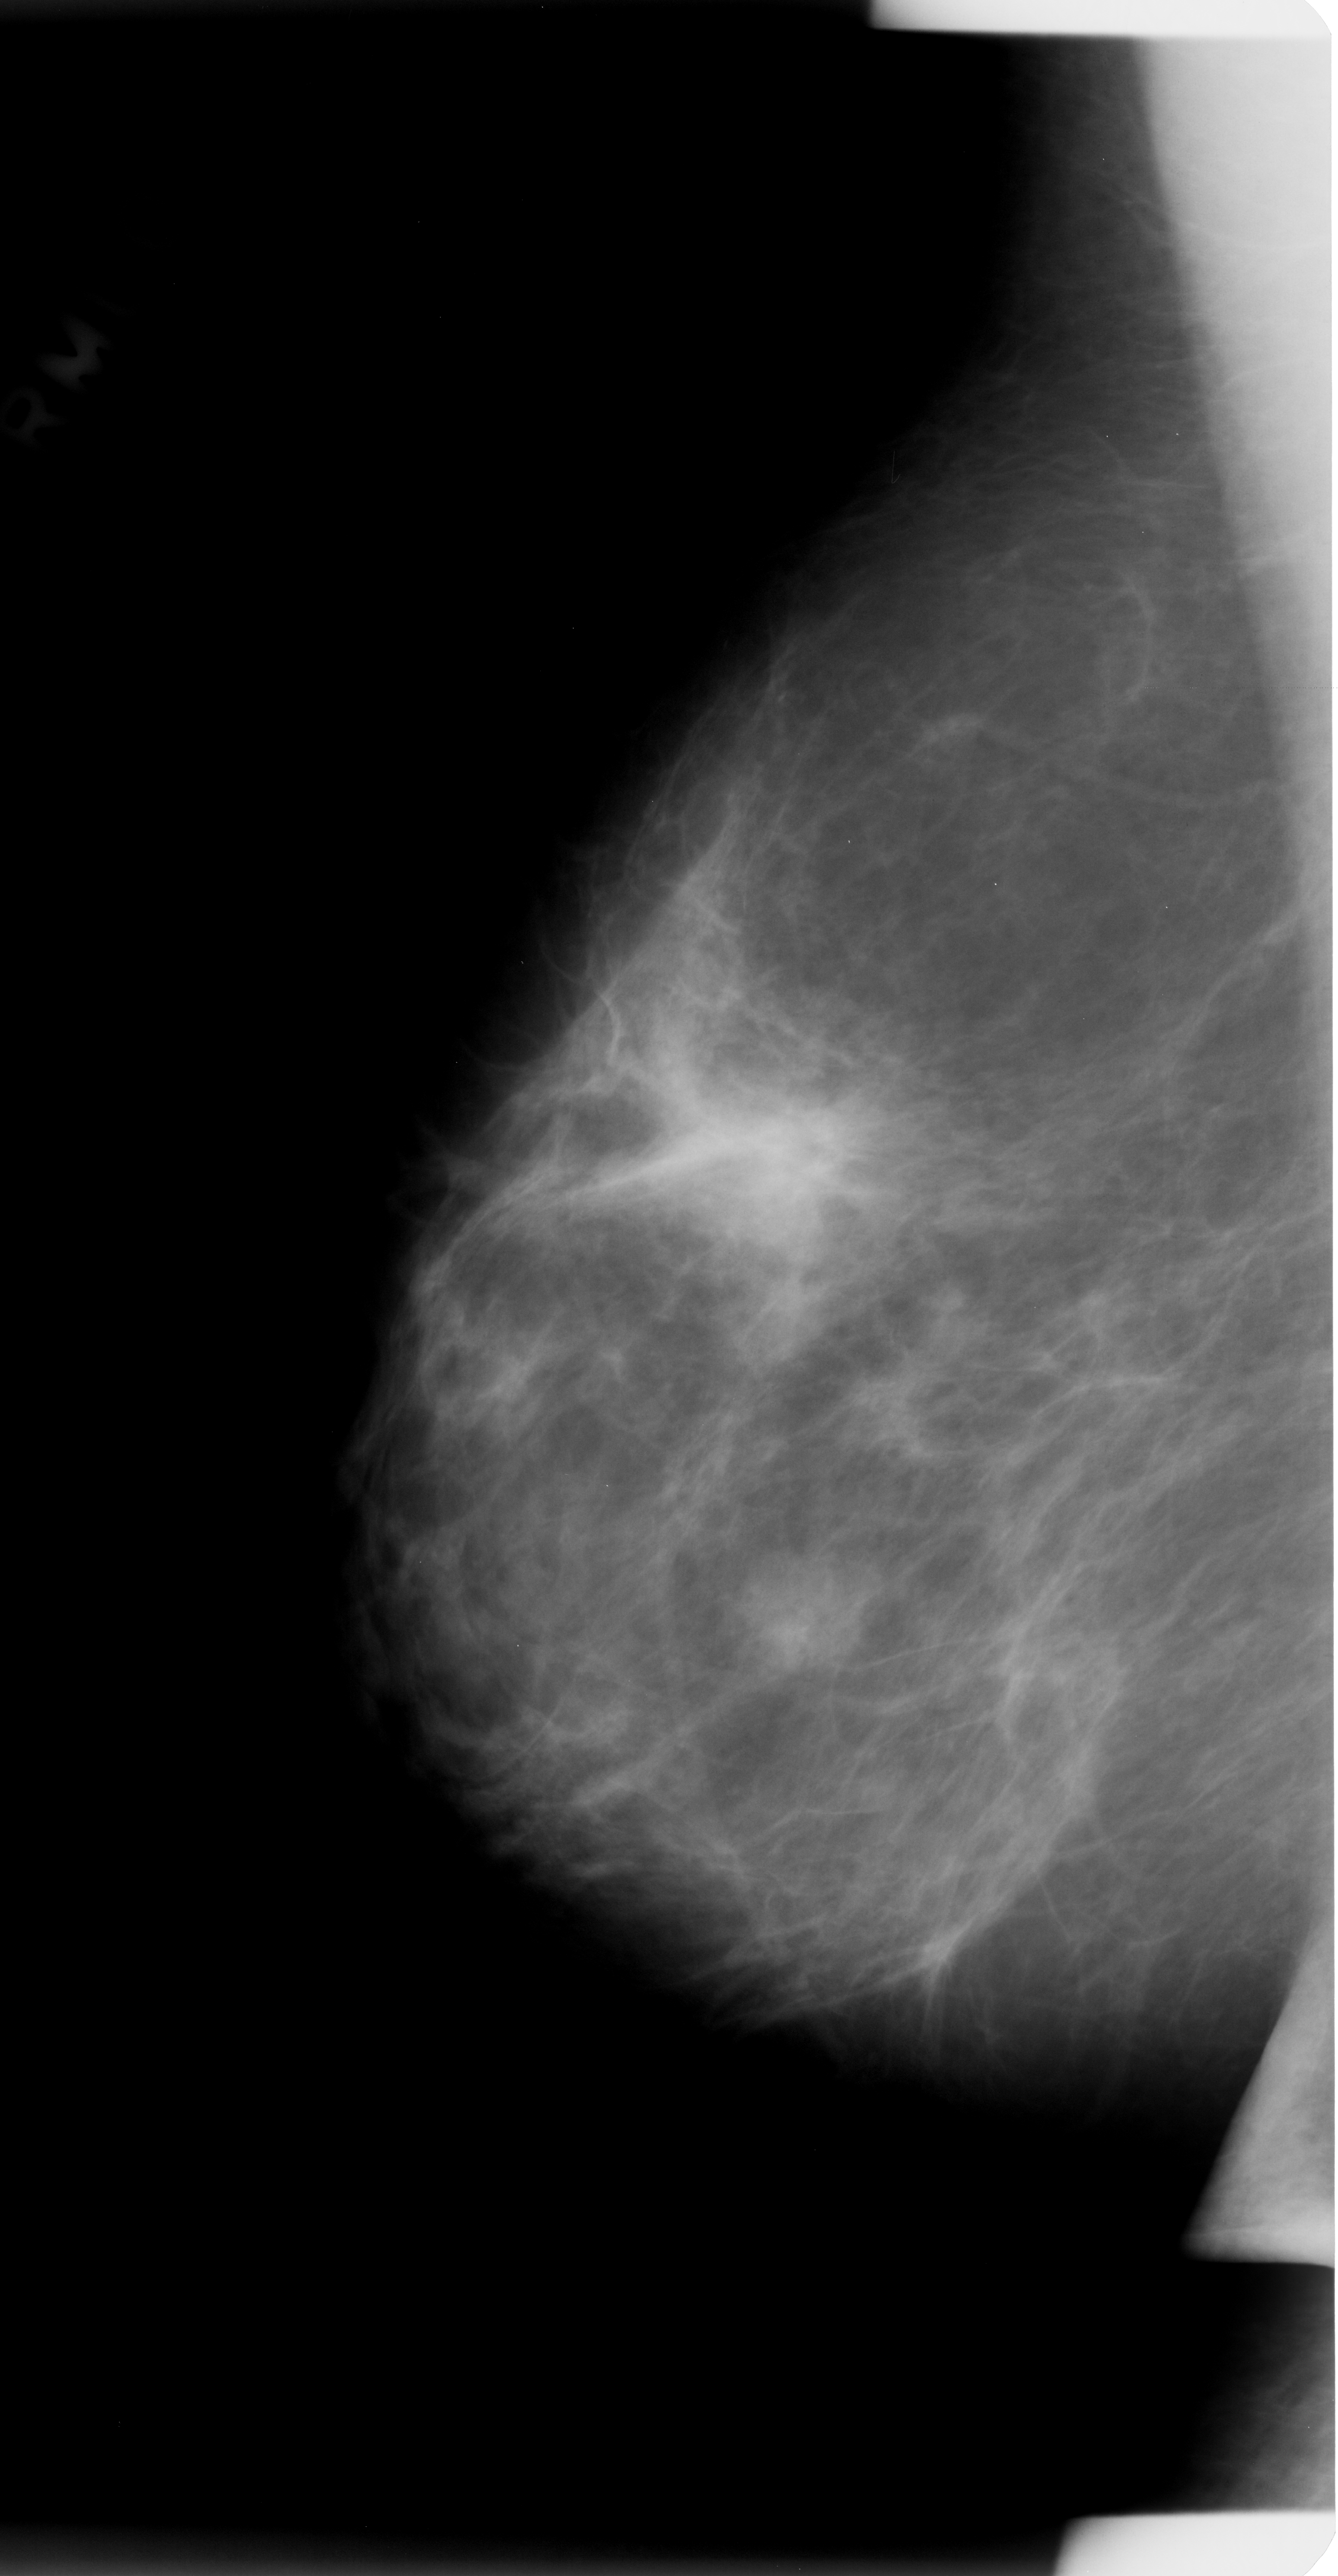
Scanned film-screen mammogram, right breast, MLO view, BI-RADS breast density category 2 (scale 1–4).
Mass, shape oval, margins microlobulated; BI-RADS assessment category 4; subtlety rating 3 on a 1 (subtle) to 5 (obvious) scale; pathology (as recorded): benign.